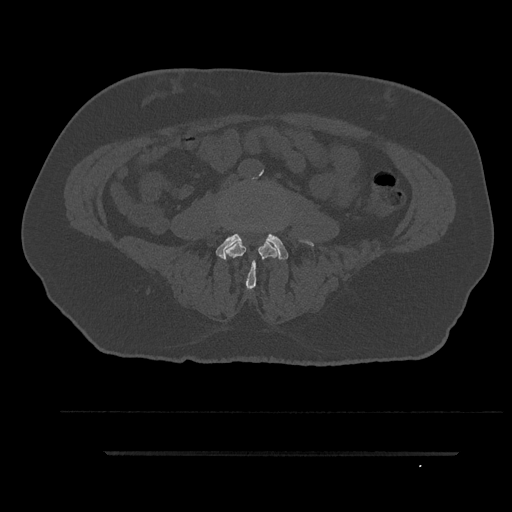
CT including the spine, one axial slice; position 3 of 797 along the scan axis; reconstruction kernel Br40s/3; 120 kVp; bone window (W 1800 / L 400 HU); 0.5 mm slice thickness; 512 × 512 image matrix, field of view 432 × 432 mm. Patient: male, 63 years. Case-level facts recorded for this patient, not image findings: primary cancer: renal; vertebrae with lytic lesions (as recorded): T8.
Structures marked on this image (semi-automatically segmented with operator editing):
- L3 vertebra: box from (x=226, y=240) to (x=278, y=289) px
- L4 vertebra: (x=216, y=234)–(x=288, y=260)